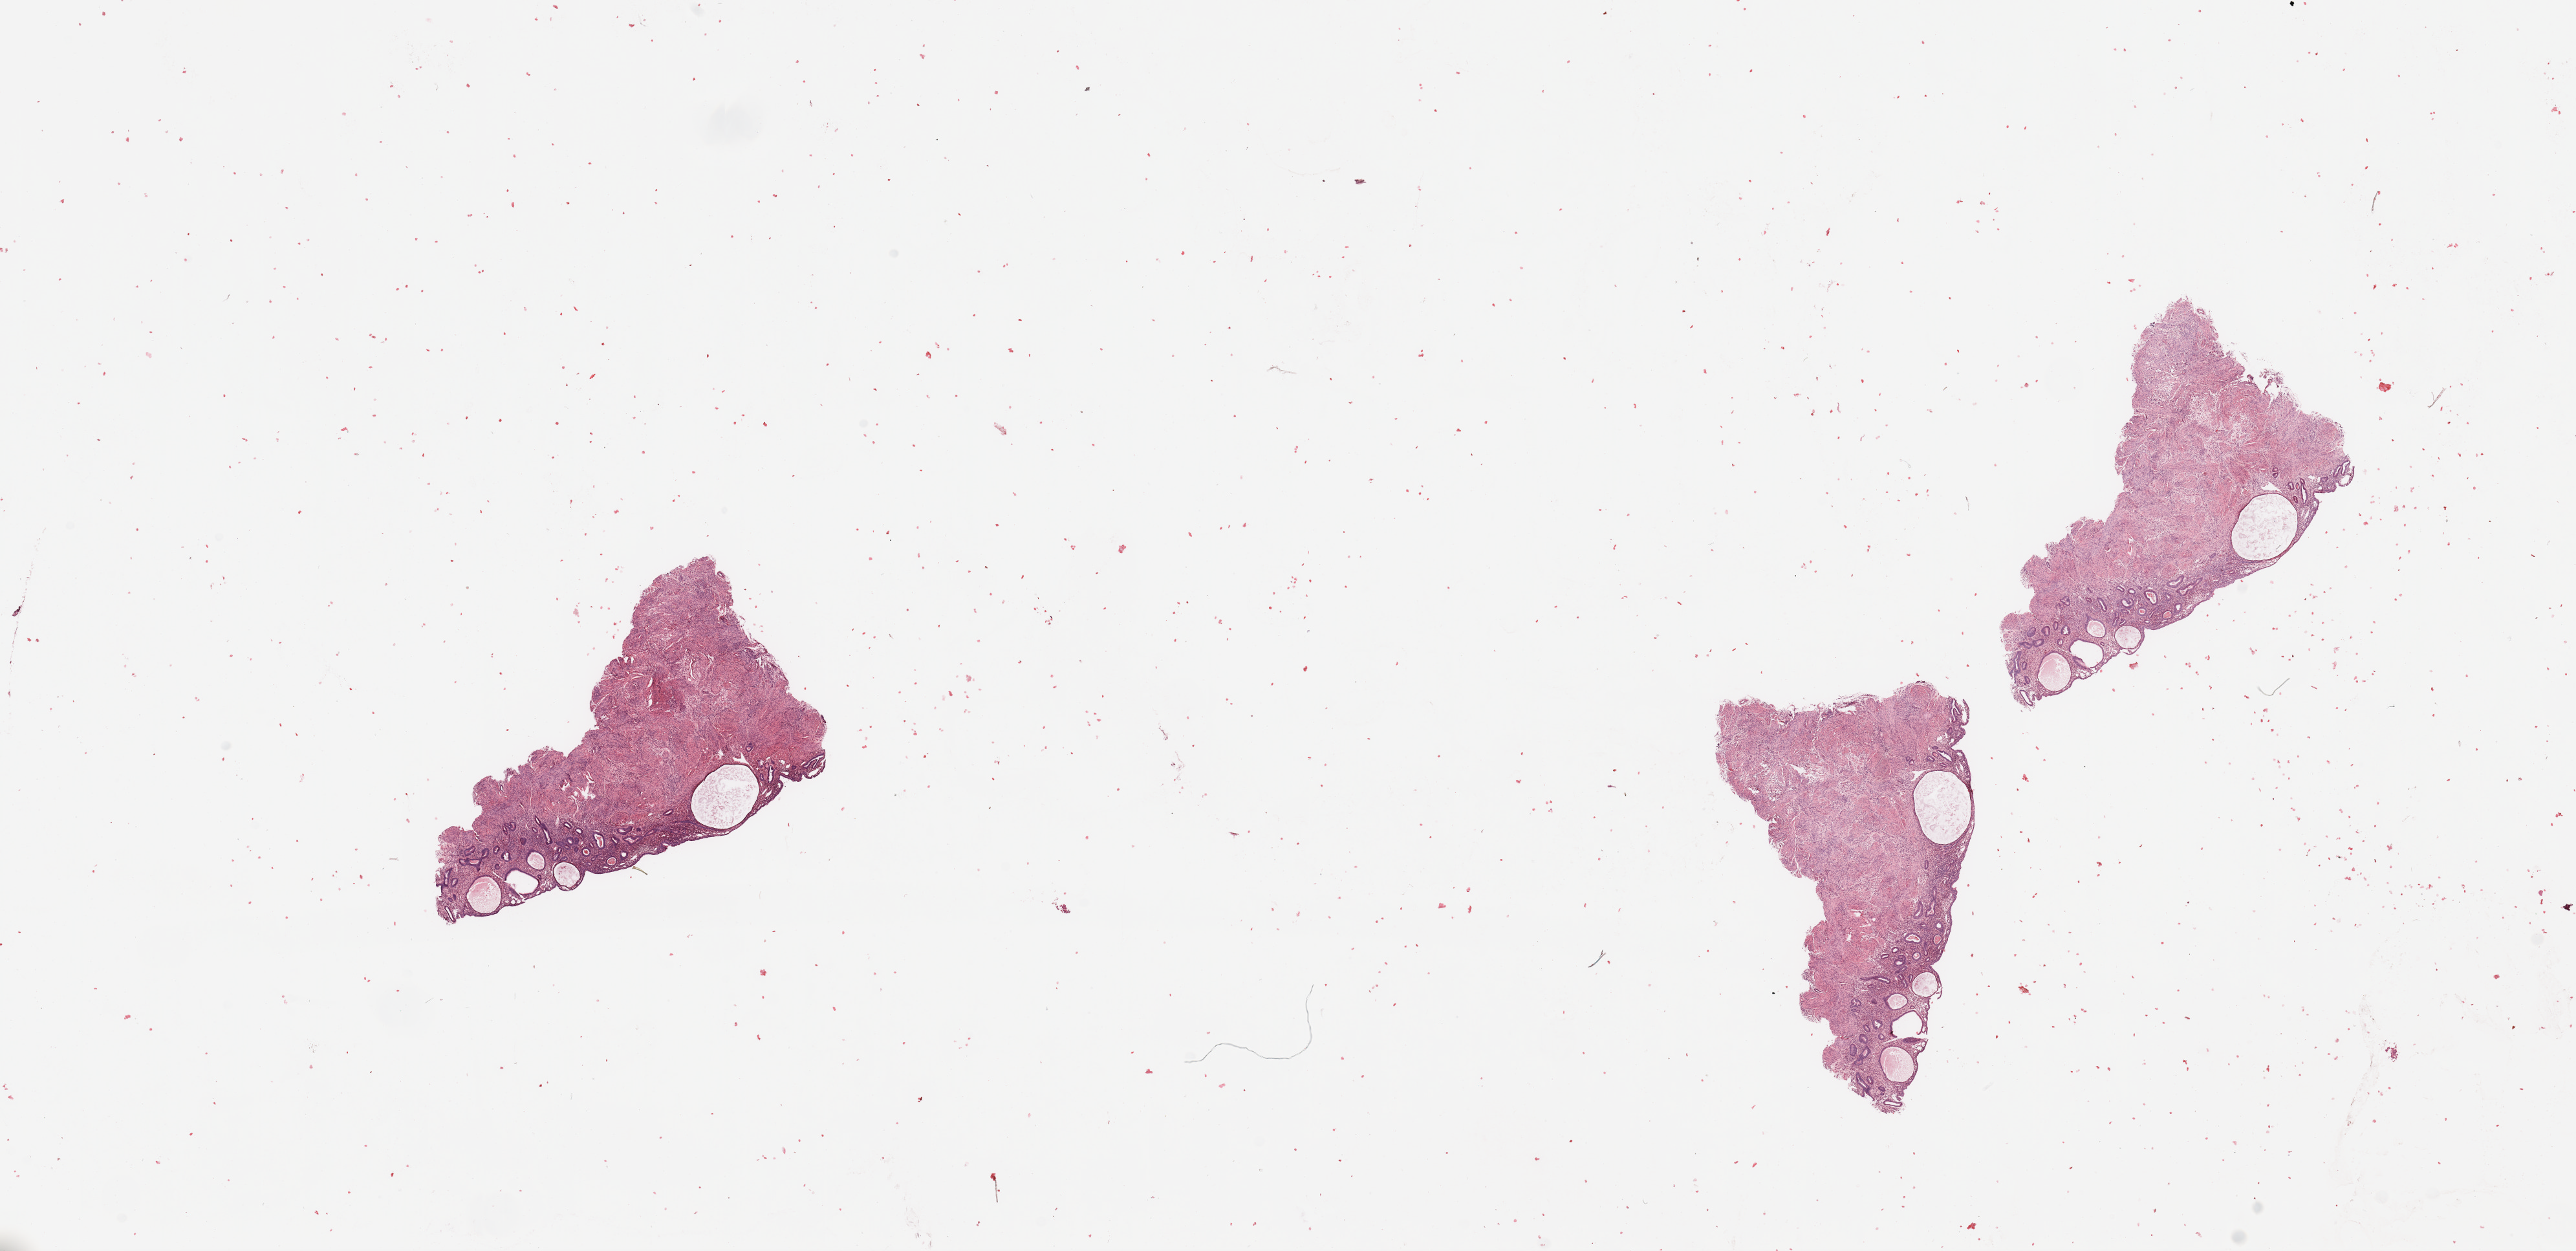
Digitized H&E tissue section (whole slide), shown as a low-resolution overview of the whole scanned area (about 31.5 x 15.3 mm, slide scanned at 20x), uterus, normal (non-tumour) tissue. 73-year-old female patient.
This section: normal (non-tumour) tissue from the same patient. Patient diagnosis: Endometrioid adenocarcinoma, NOS.